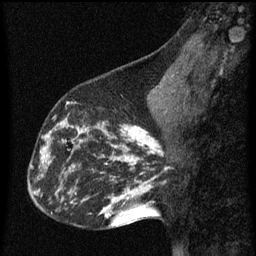
Breast MRI (dynamic contrast-enhanced), one sagittal slice; position 25 of 60 along the scan axis; dynamic contrast-enhanced series, image 2 of 3 at this slice position (ordered by acquisition); 1.5 T; TE 4.2 ms, TR 8 ms; 2 mm slice thickness; 256 × 256 image matrix, field of view 180 × 180 mm. Female patient, age 43 years.
Structures marked on this image (semi-automatic segmentation, software-assisted and operator-edited):
- analysis volume of interest (the breast-tissue region the enhancement analysis was run in; not a lesion): bounding box [x1, y1, x2, y2] px = [53, 104, 101, 155]
- tumour enhancement mask (voxels above the 70 % enhancement threshold inside the analysis volume of interest): [54, 104, 101, 147]